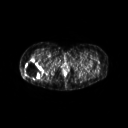
FDG PET of an extremity soft-tissue mass (from a PET/CT study), one axial slice. Position 35 of 267 along the scan axis. 3.27 mm slice thickness. 128 × 128 image matrix, field of view 600 × 600 mm. Patient: female, 57 years. Case-level facts recorded for this patient, not image findings: histological type: epithelioid sarcoma with vascular differentiation; site of the primary tumour: right buttock.
Annotated regions visible in this slice (expert contour drawn on MRI and transferred to this co-registered scan by the dataset authors):
- gross tumour volume (mass): box from (x=24, y=59) to (x=43, y=79) px